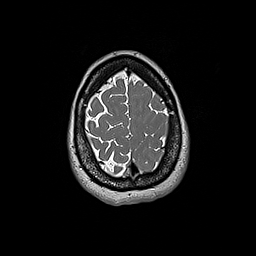
Brain MRI from a brain-tumour surgery series, one axial slice; position 48 of 192 along the scan axis; 1 mm slice thickness; 256 × 256 image matrix, field of view 250 × 250 mm. Case-level facts recorded for this patient, not image findings: histopathology: Glioblastoma; WHO grade: 4; IDH mutation: no.
Outlined on this slice (outlined manually by an expert reader):
- tumour: bounding box <160,136,169,156> (left, top, right, bottom; pixels)